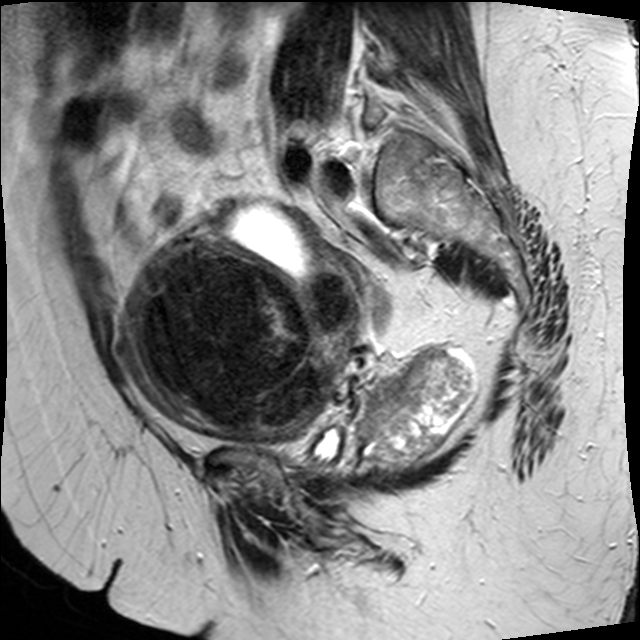
Pelvic MRI for cervical cancer, one sagittal slice; slice 12 of 34 in the series (ordered by position); T2-weighted; 1.5 T; TE 89 ms, TR 3320 ms; 4 mm slice thickness; 640 × 640 image matrix. Patient: female, 50 years.
Structures marked on this image (expert manual segmentation):
- uterus and cervix: bounding box (x1, y1, x2, y2) in pixels: (120, 200, 476, 477)